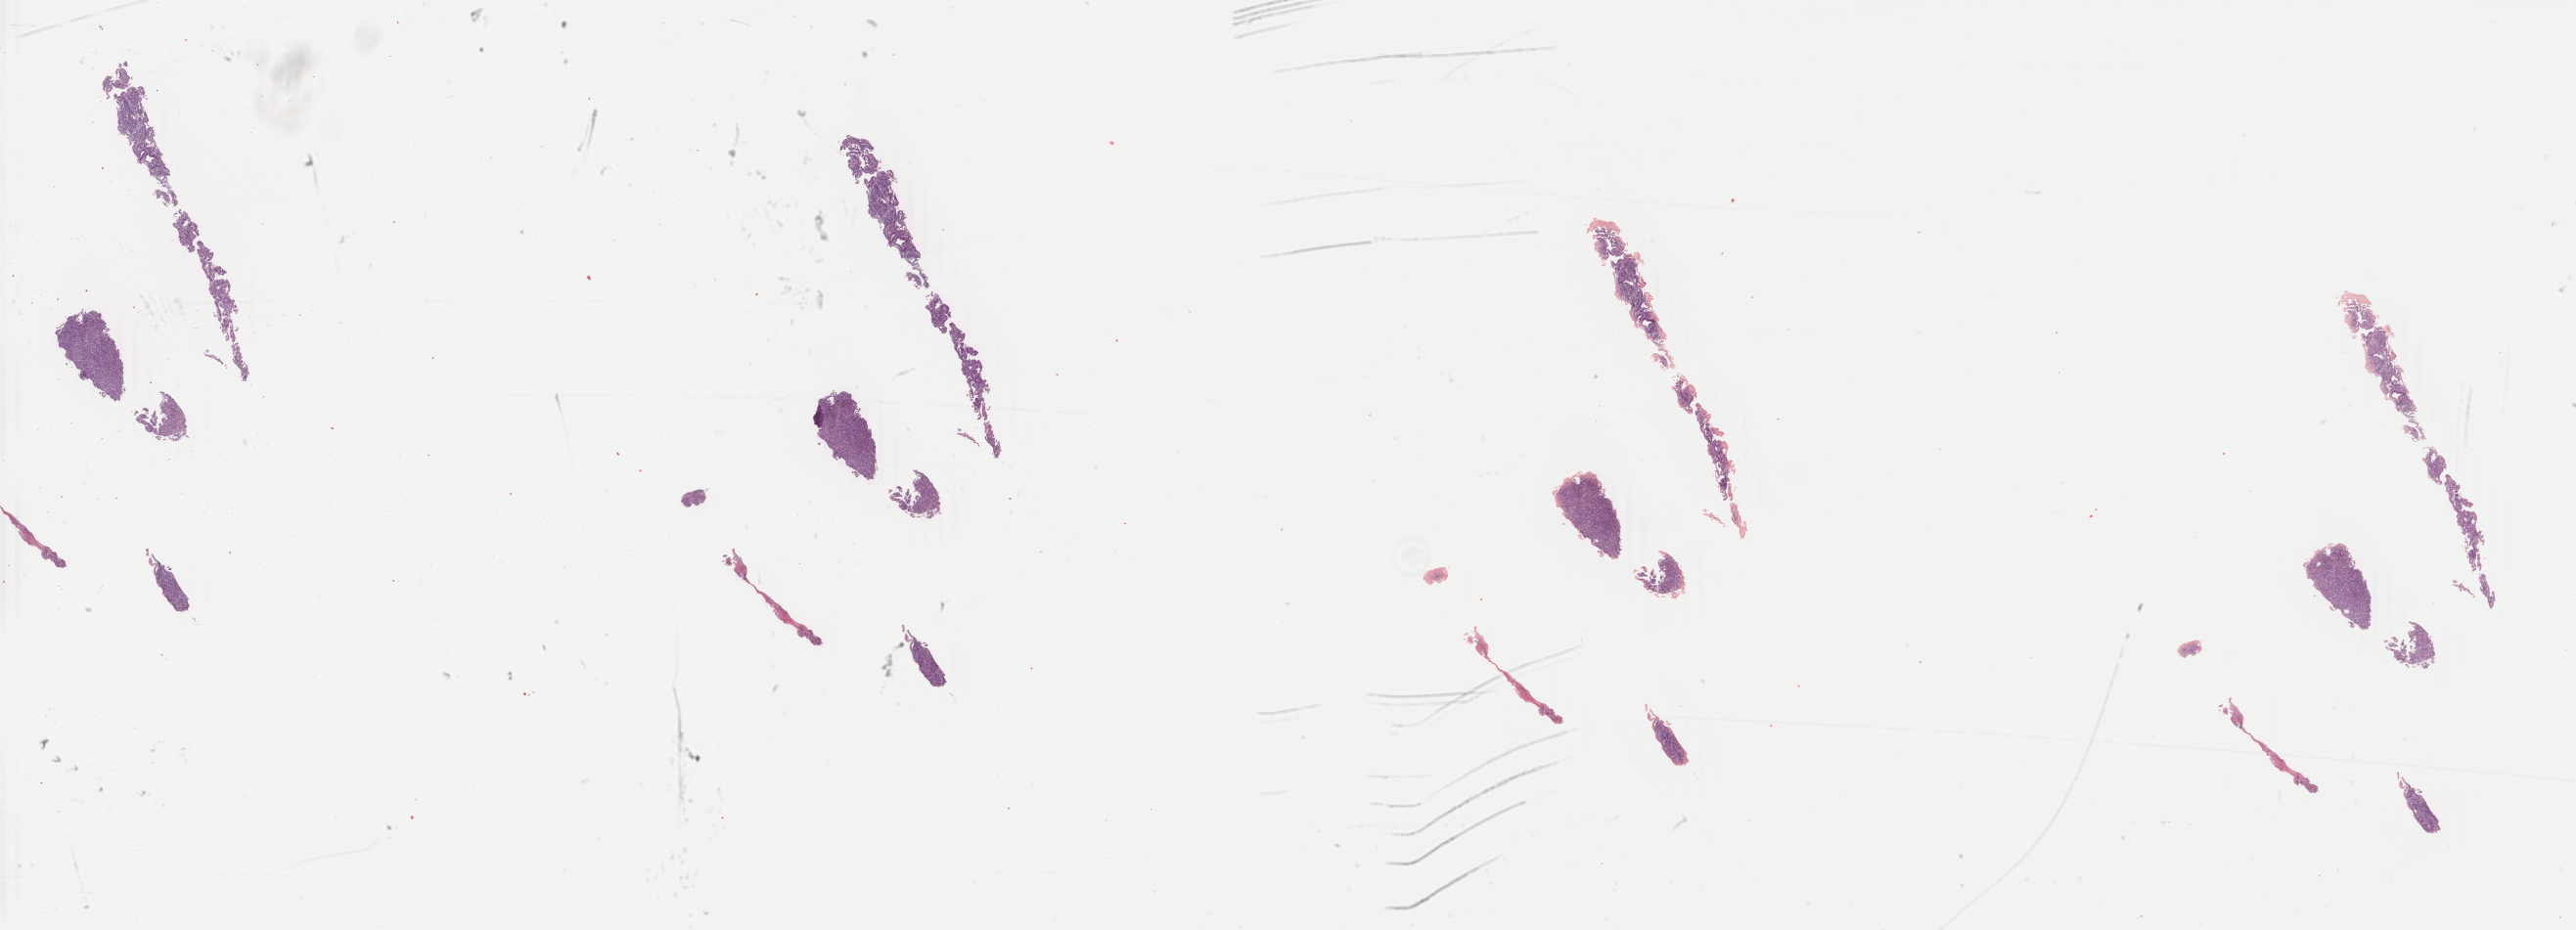
H&E whole-slide image, a low-resolution overview of the entire scanned area, about 41.9 x 15.1 mm (slide scanned at 40x); formalin-fixed paraffin-embedded (FFPE) diagnostic section; stomach, primary tumour sample. Female, age 70 years at initial diagnosis.
Pathologic diagnosis: Tubular adenocarcinoma (body of stomach).